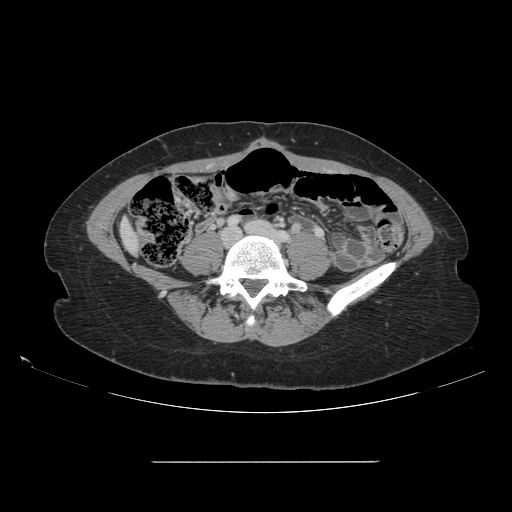
Contrast-enhanced abdominal CT, one axial slice. Position 7 of 151 along the scan axis. Soft-tissue window (W 400 / L 40 HU). 2.5 mm slice thickness. 512 × 512 image matrix. Female patient, age 46 years. From the clinical record (not read from this slice): diagnosis: colorectal cancer liver metastases, imaged before liver resection.
Structures marked on this image (expert manual segmentation):
- liver: bounding box [x1, y1, x2, y2] px = [123, 225, 138, 249]
- planned liver remnant (the part of the liver to remain after resection): [122, 224, 137, 249]